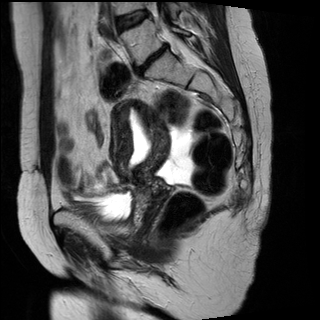
Pelvic MRI for cervical cancer, one sagittal slice. Position 18 of 29 along the scan axis. T2-weighted. 1.5 T. TE 89 ms, TR 2930 ms. 4 mm slice thickness. 320 × 320 image matrix. Female patient, age 45 years.
Annotated regions visible in this slice (expert manual segmentation):
- uterus and cervix: bounding box [x1, y1, x2, y2] px = [111, 99, 172, 198]